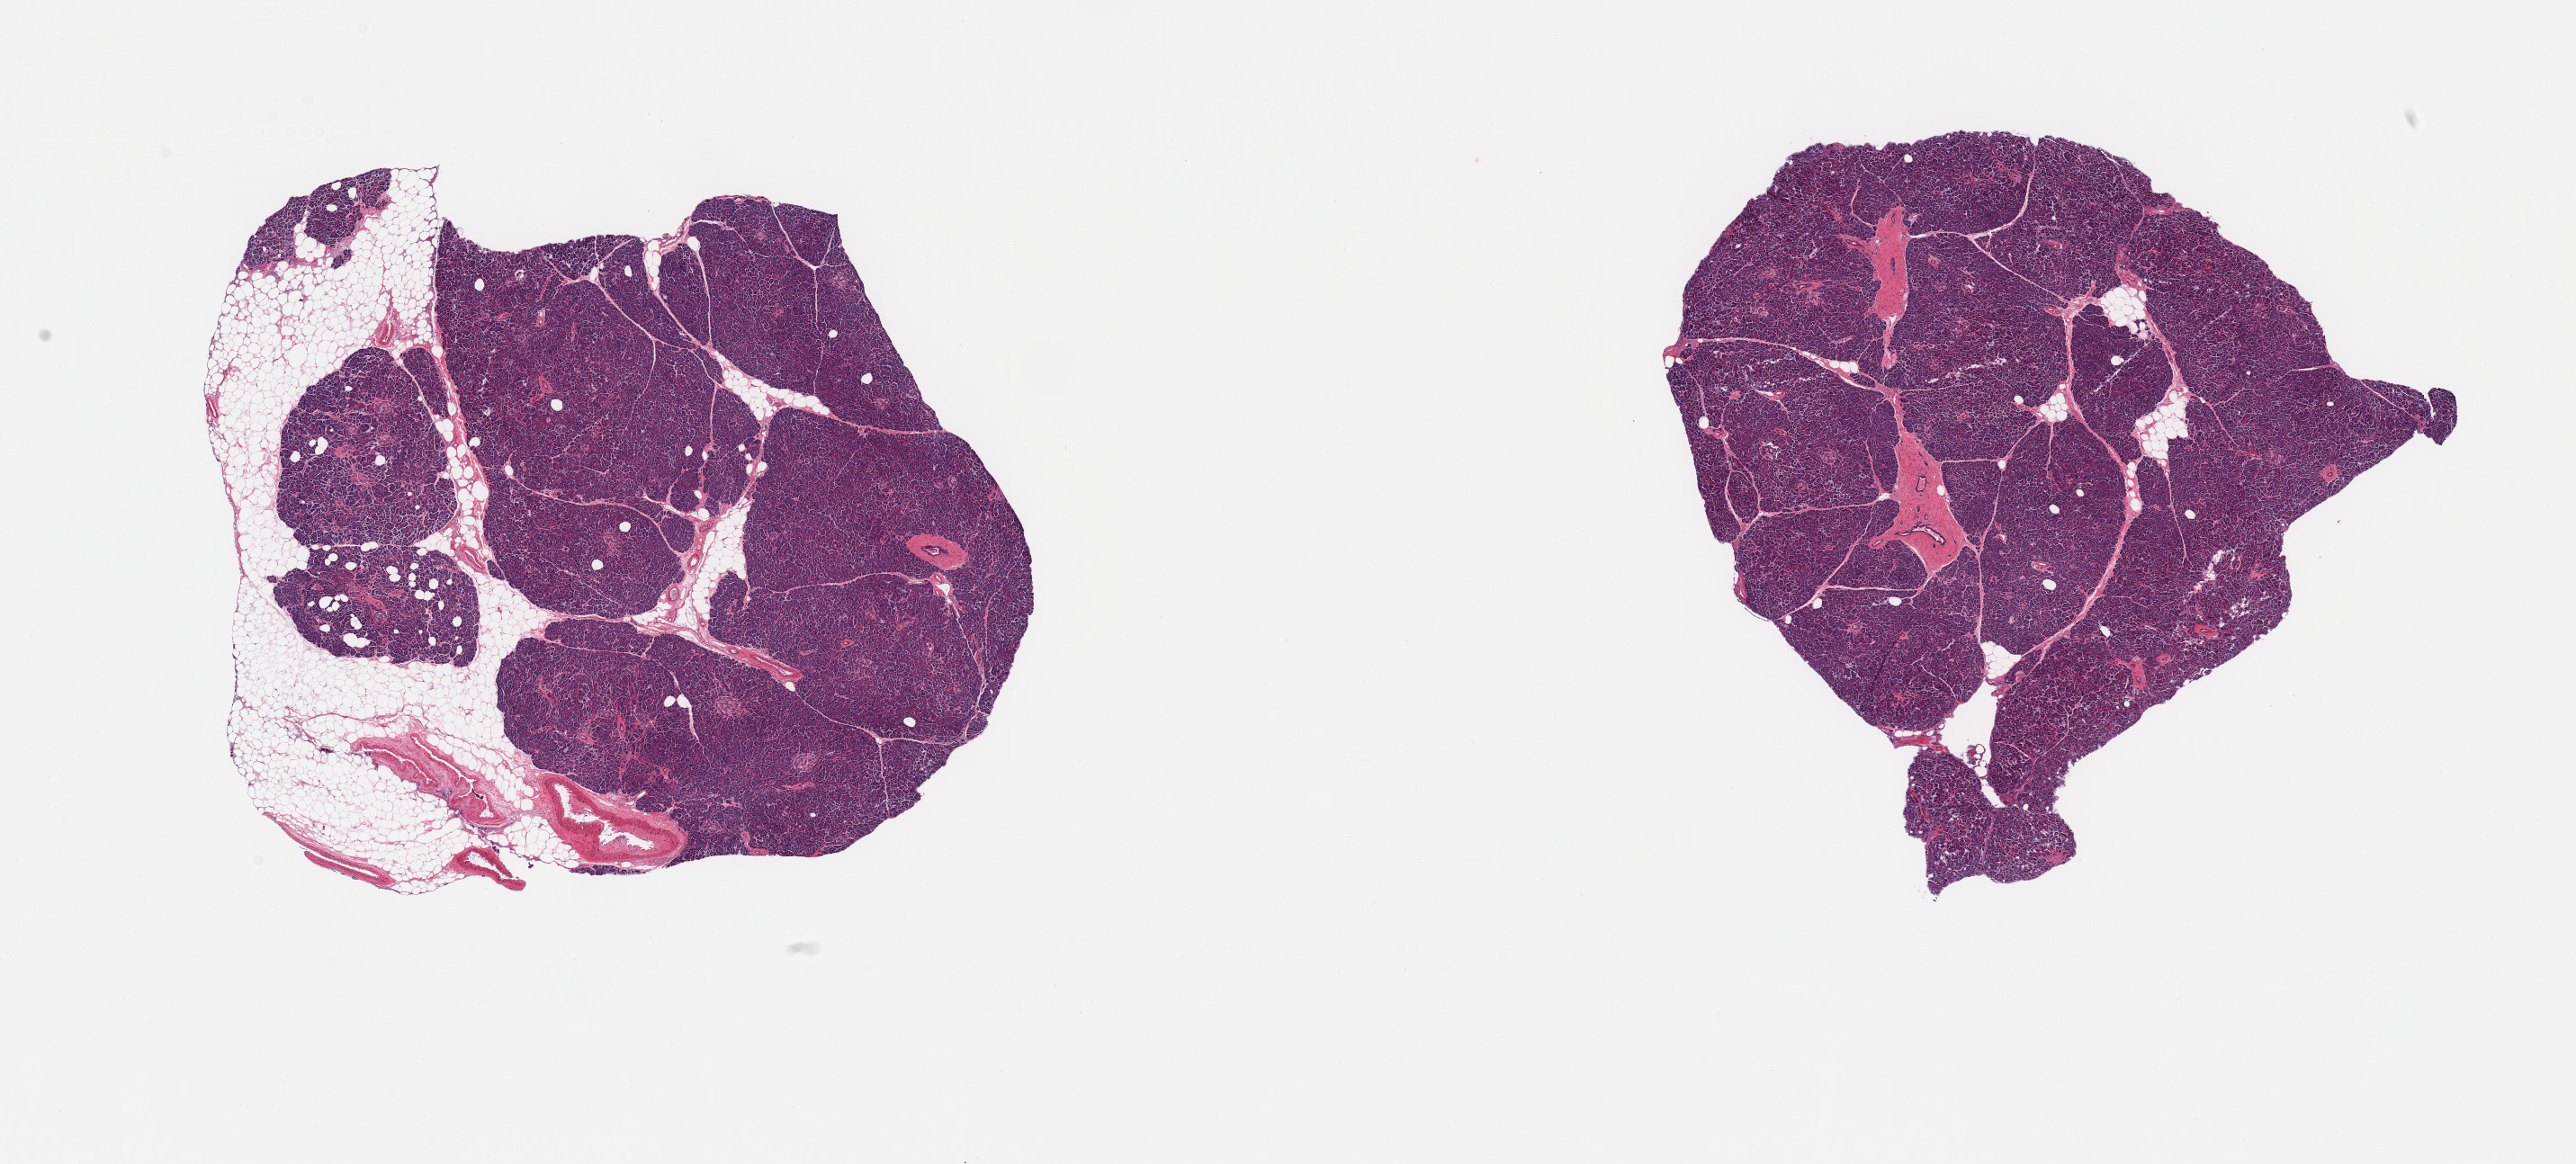
Haematoxylin and eosin whole-slide image, shown as a low-resolution overview of the whole scanned area (about 22.6 x 10.2 mm, from a 20x scan); PAXgene-fixed, paraffin-embedded tissue; target tissue: pancreas; tissue donor sample. Male donor.
• reviewer comment on this tissue sample: 2 pieces; well preserved parenchyma with Langerhans islets; 30% and 5% internal/external fat